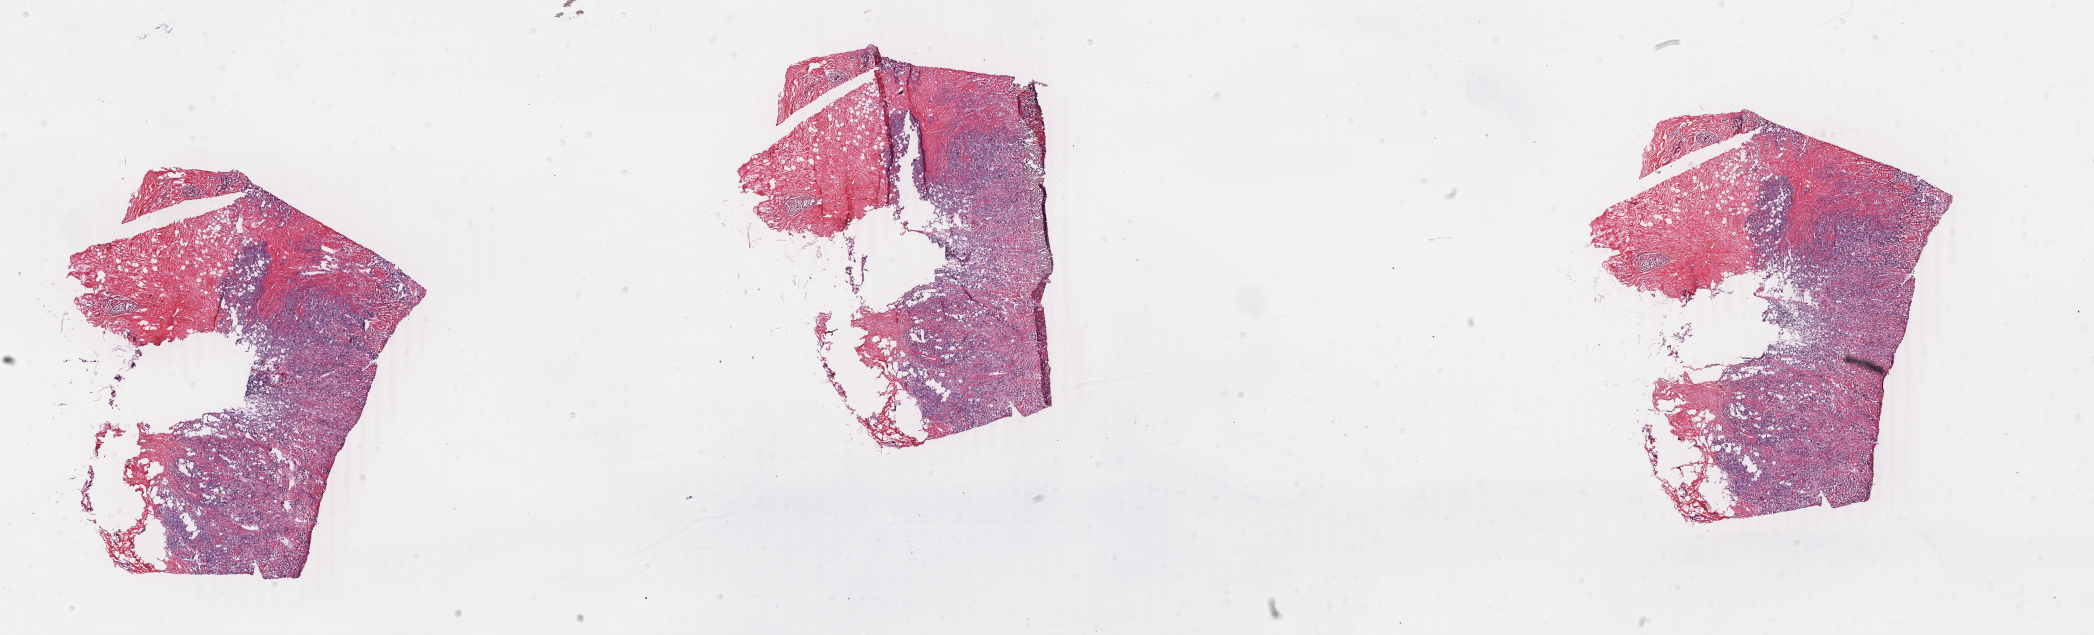
H&E whole-slide image — whole scanned area (about 33.3 x 10.1 mm) shown as a low-resolution overview. Frozen section from the bottom of the tissue portion. Primary tumour sample from the breast. Female patient; age at initial diagnosis 61 years. Composition of this section per pathologist review: tumour cells 85%, tumour nuclei 85%, normal cells 2%, stromal cells 12%, necrosis 1%. Infiltration values recorded for this section: lymphocyte infiltration 1%, monocyte infiltration 0%, neutrophil infiltration 0%.
* pathologic diagnosis: Lobular carcinoma, NOS
* AJCC pathologic stage: IIA
* lymph nodes positive (case pathology): 0 of 2 examined